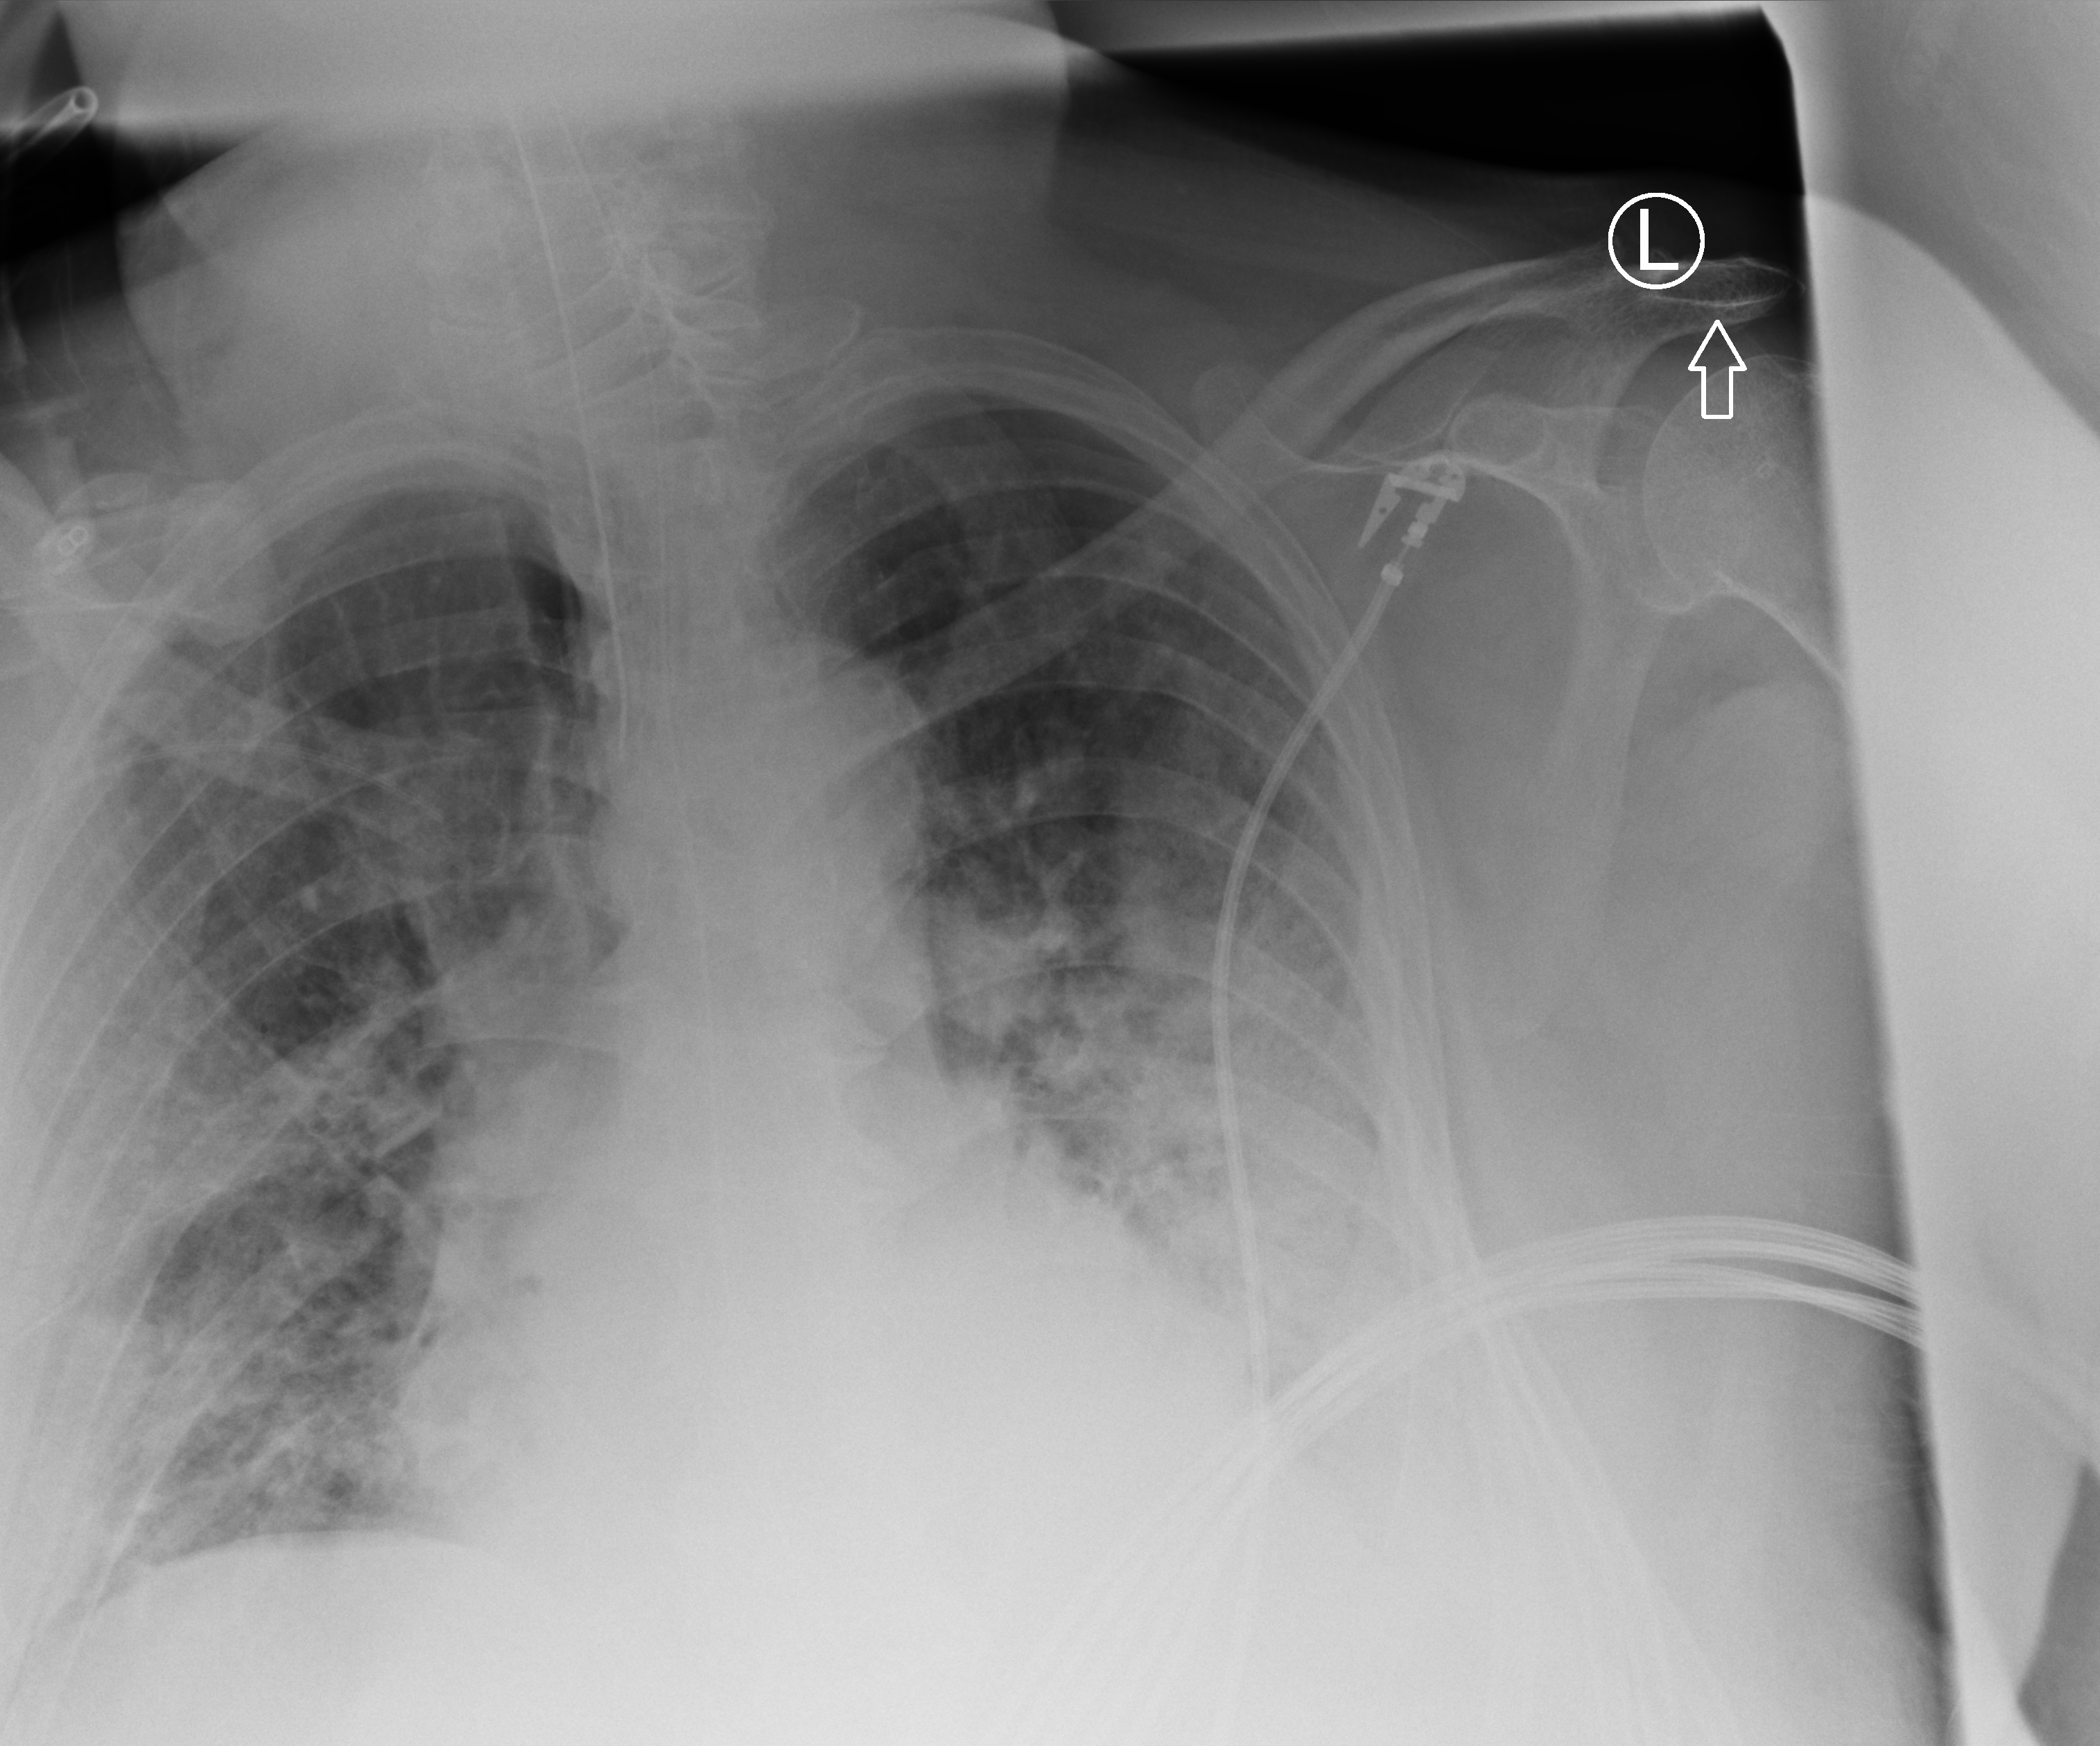
Chest X-ray (portable), anteroposterior (AP) projection. Male patient hospitalised with COVID-19, age 60–74 years.
From the hospital-stay record, not from the radiograph (when in the stay this image was taken is not recorded): mechanically ventilated during this hospital stay: yes; chronic kidney disease (admission record): no.